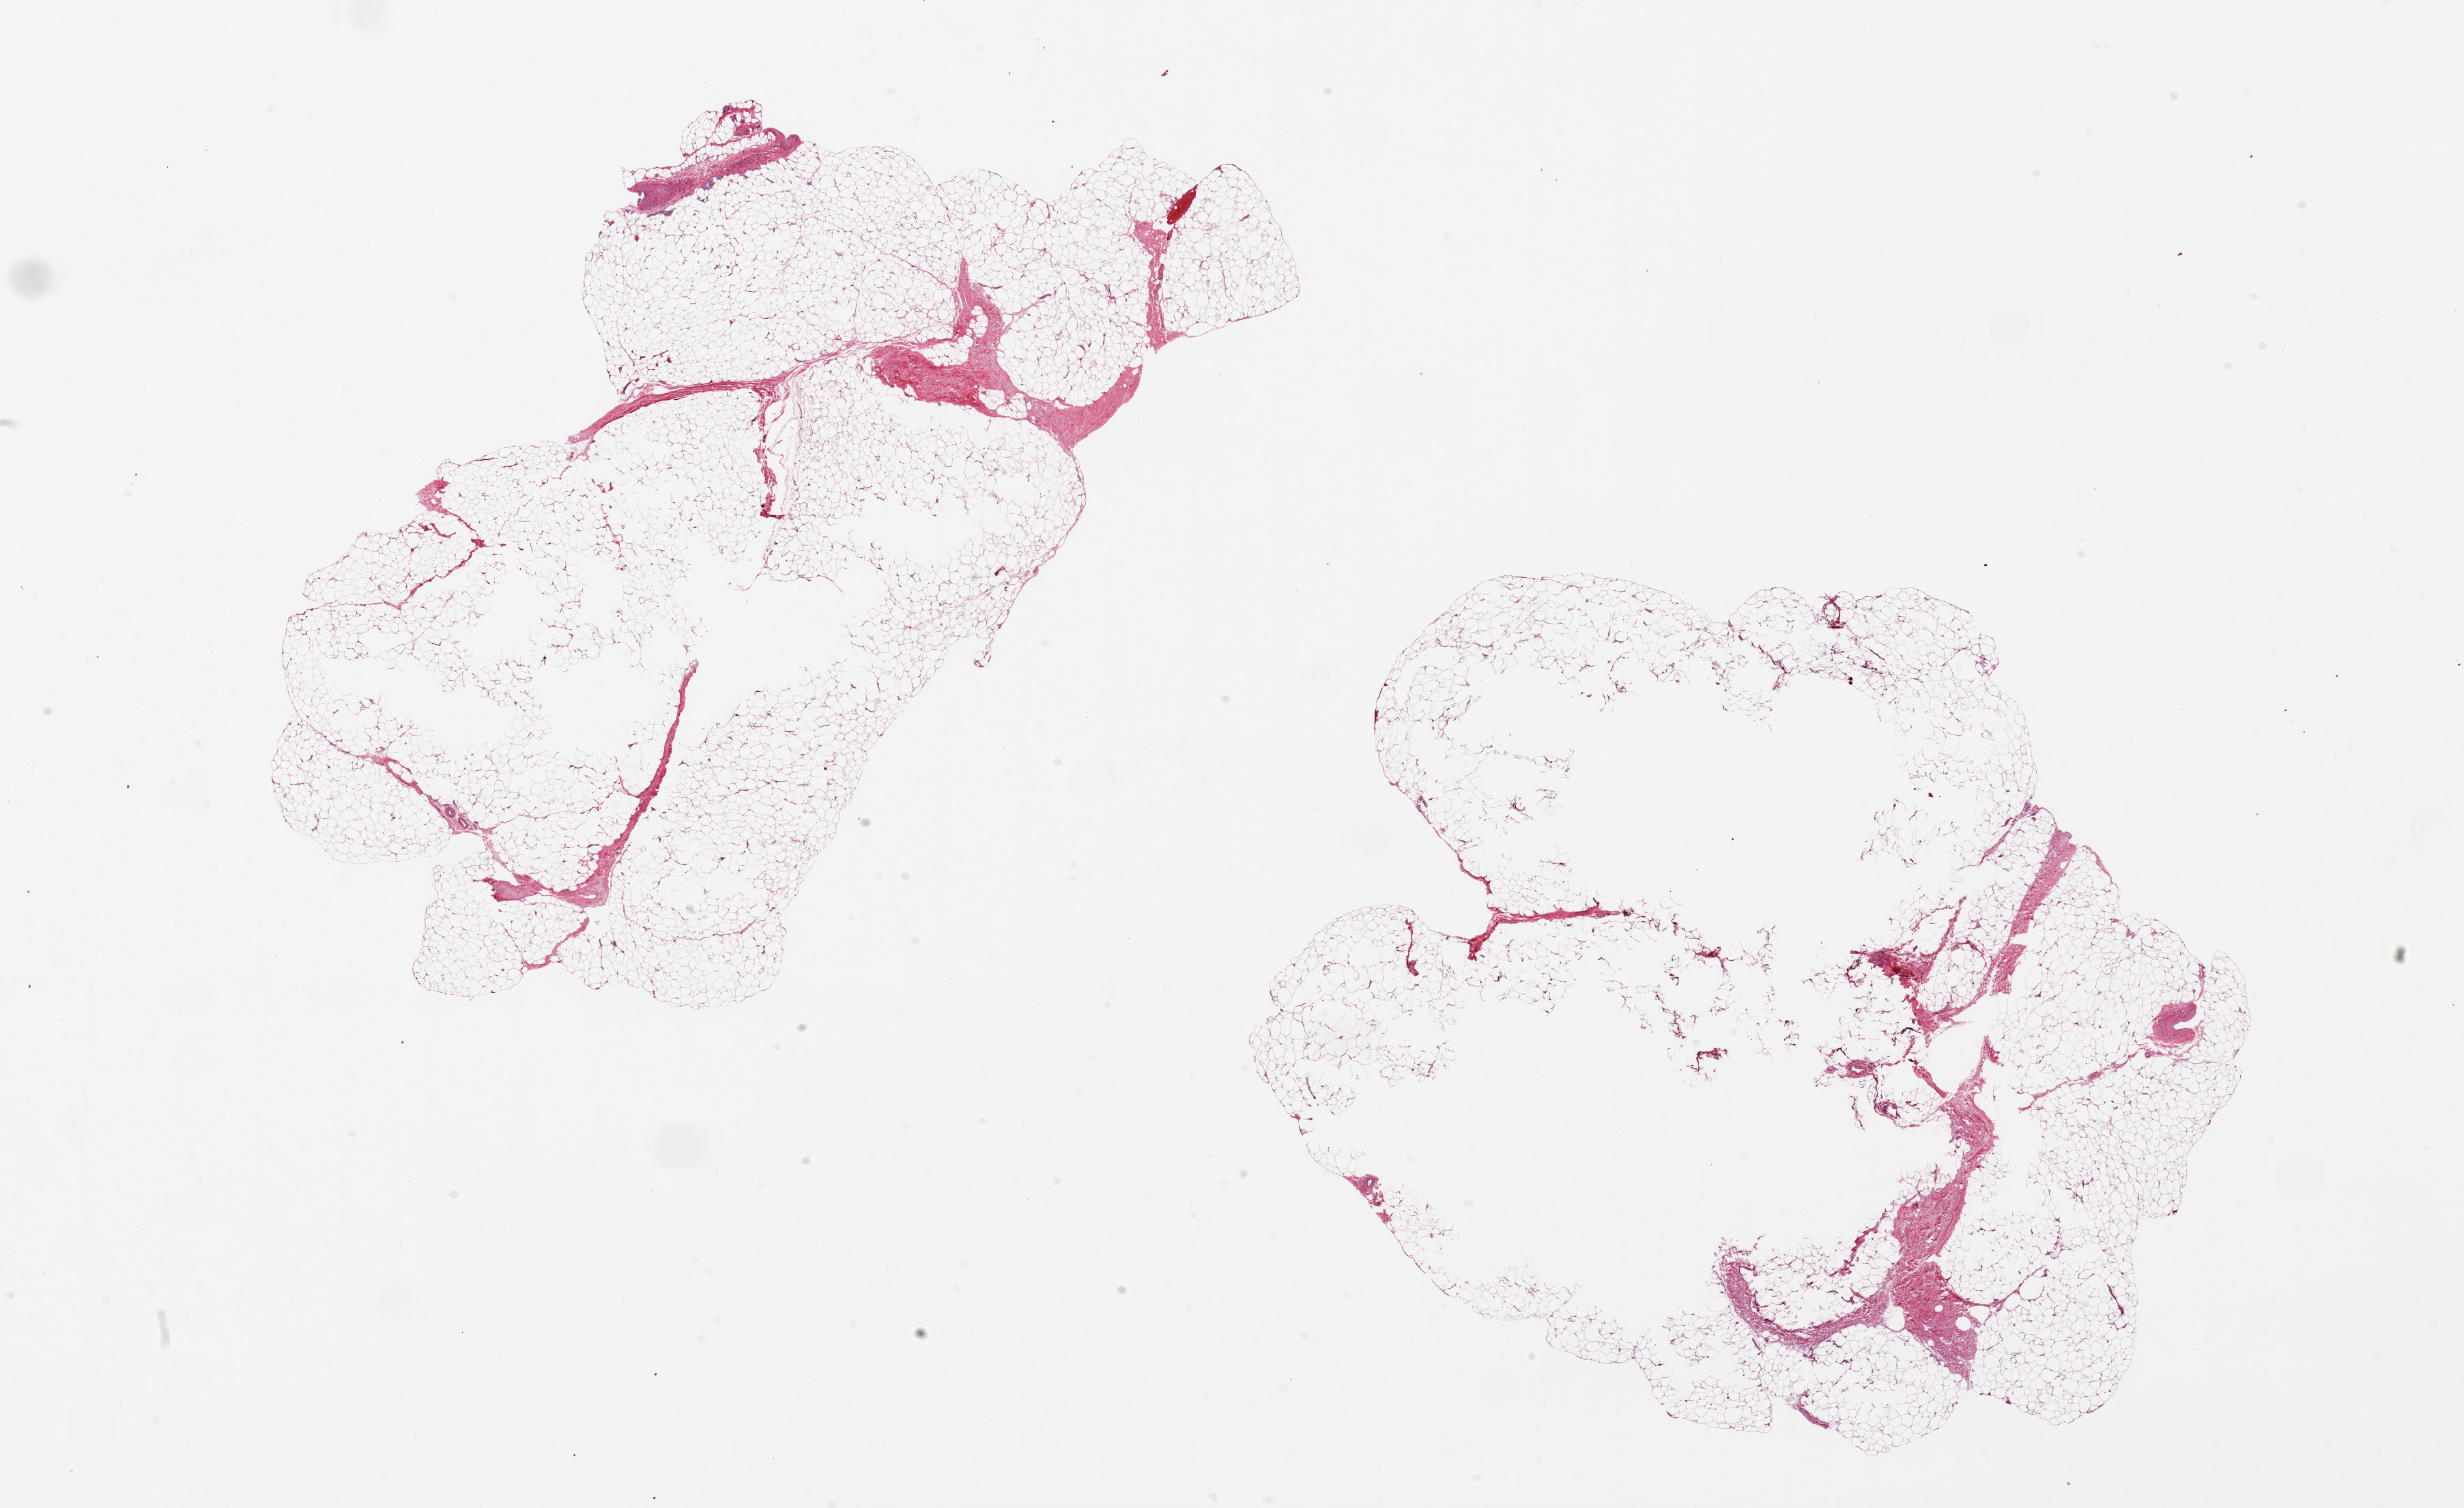
Digitized haematoxylin and eosin-stained section, brightfield — shown as a low-resolution overview of the whole scanned area (about 28.5 x 17.5 mm, acquisition: 20x scan), PAXgene-fixed paraffin-embedded (PFPE) section, section of adipose tissue (target tissue), donor tissue sample.
Review note (as recorded): 2 pieces 13x6 & 11x8 mm; central holes in large aliquots.